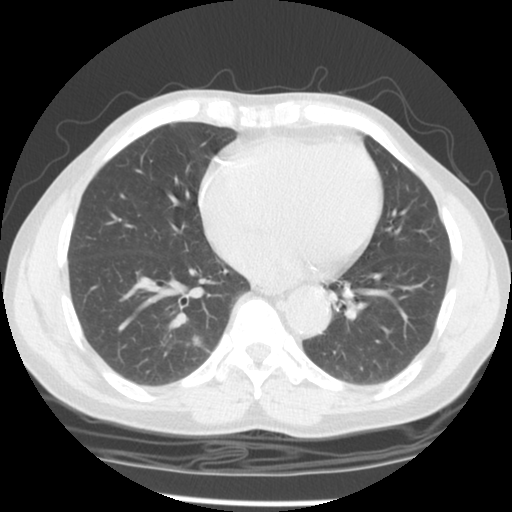
Low-dose screening chest CT, one axial slice; position 54 of 127 along the scan axis; lung window (W 1500 / L -600 HU); 2.5 mm slice thickness; 512 × 512 image matrix, field of view 320 × 320 mm.
Outlined on this slice (manually delineated by an expert):
- lesion 1 (tumor, lower lobe of right lung): box from (x=193, y=336) to (x=201, y=346) px